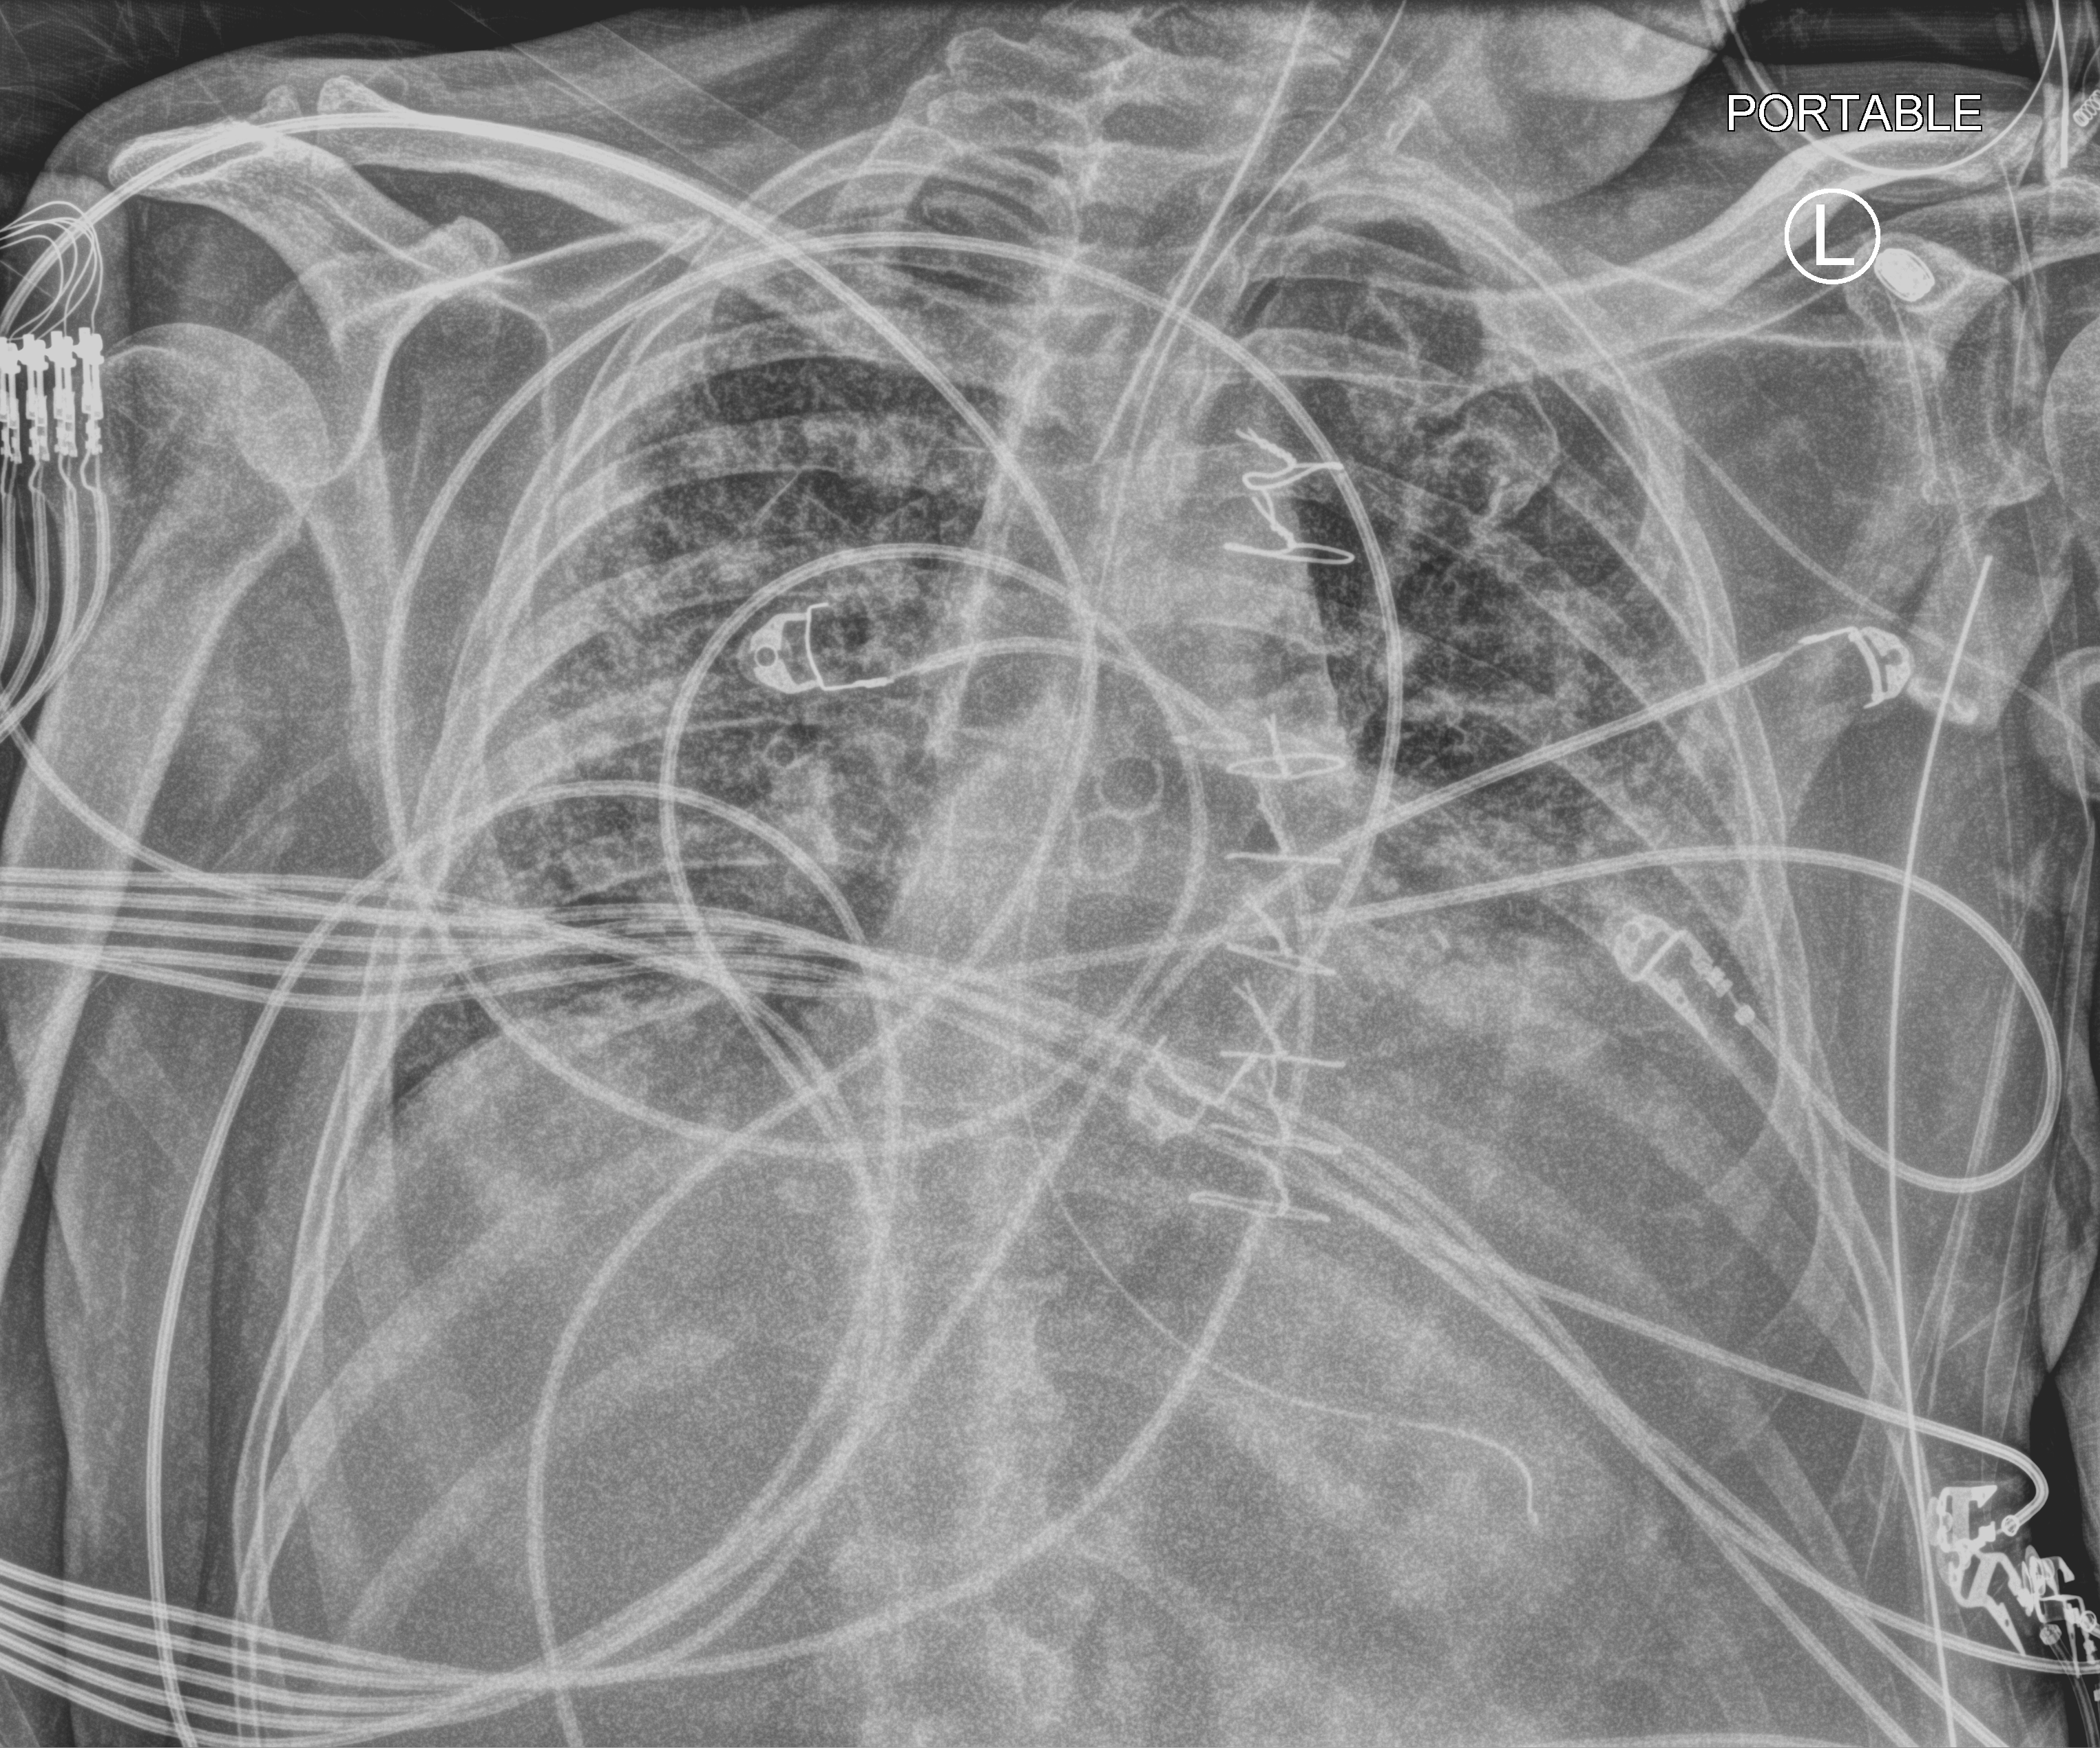
Chest X-ray (portable), anteroposterior (AP) projection. Patient hospitalised with COVID-19; male, aged 18–59 years.
Hospital-stay facts (about this admission, not read from this image; timing relative to this image not recorded): admitted to intensive care during this hospital stay: yes; COPD (admission record): yes.